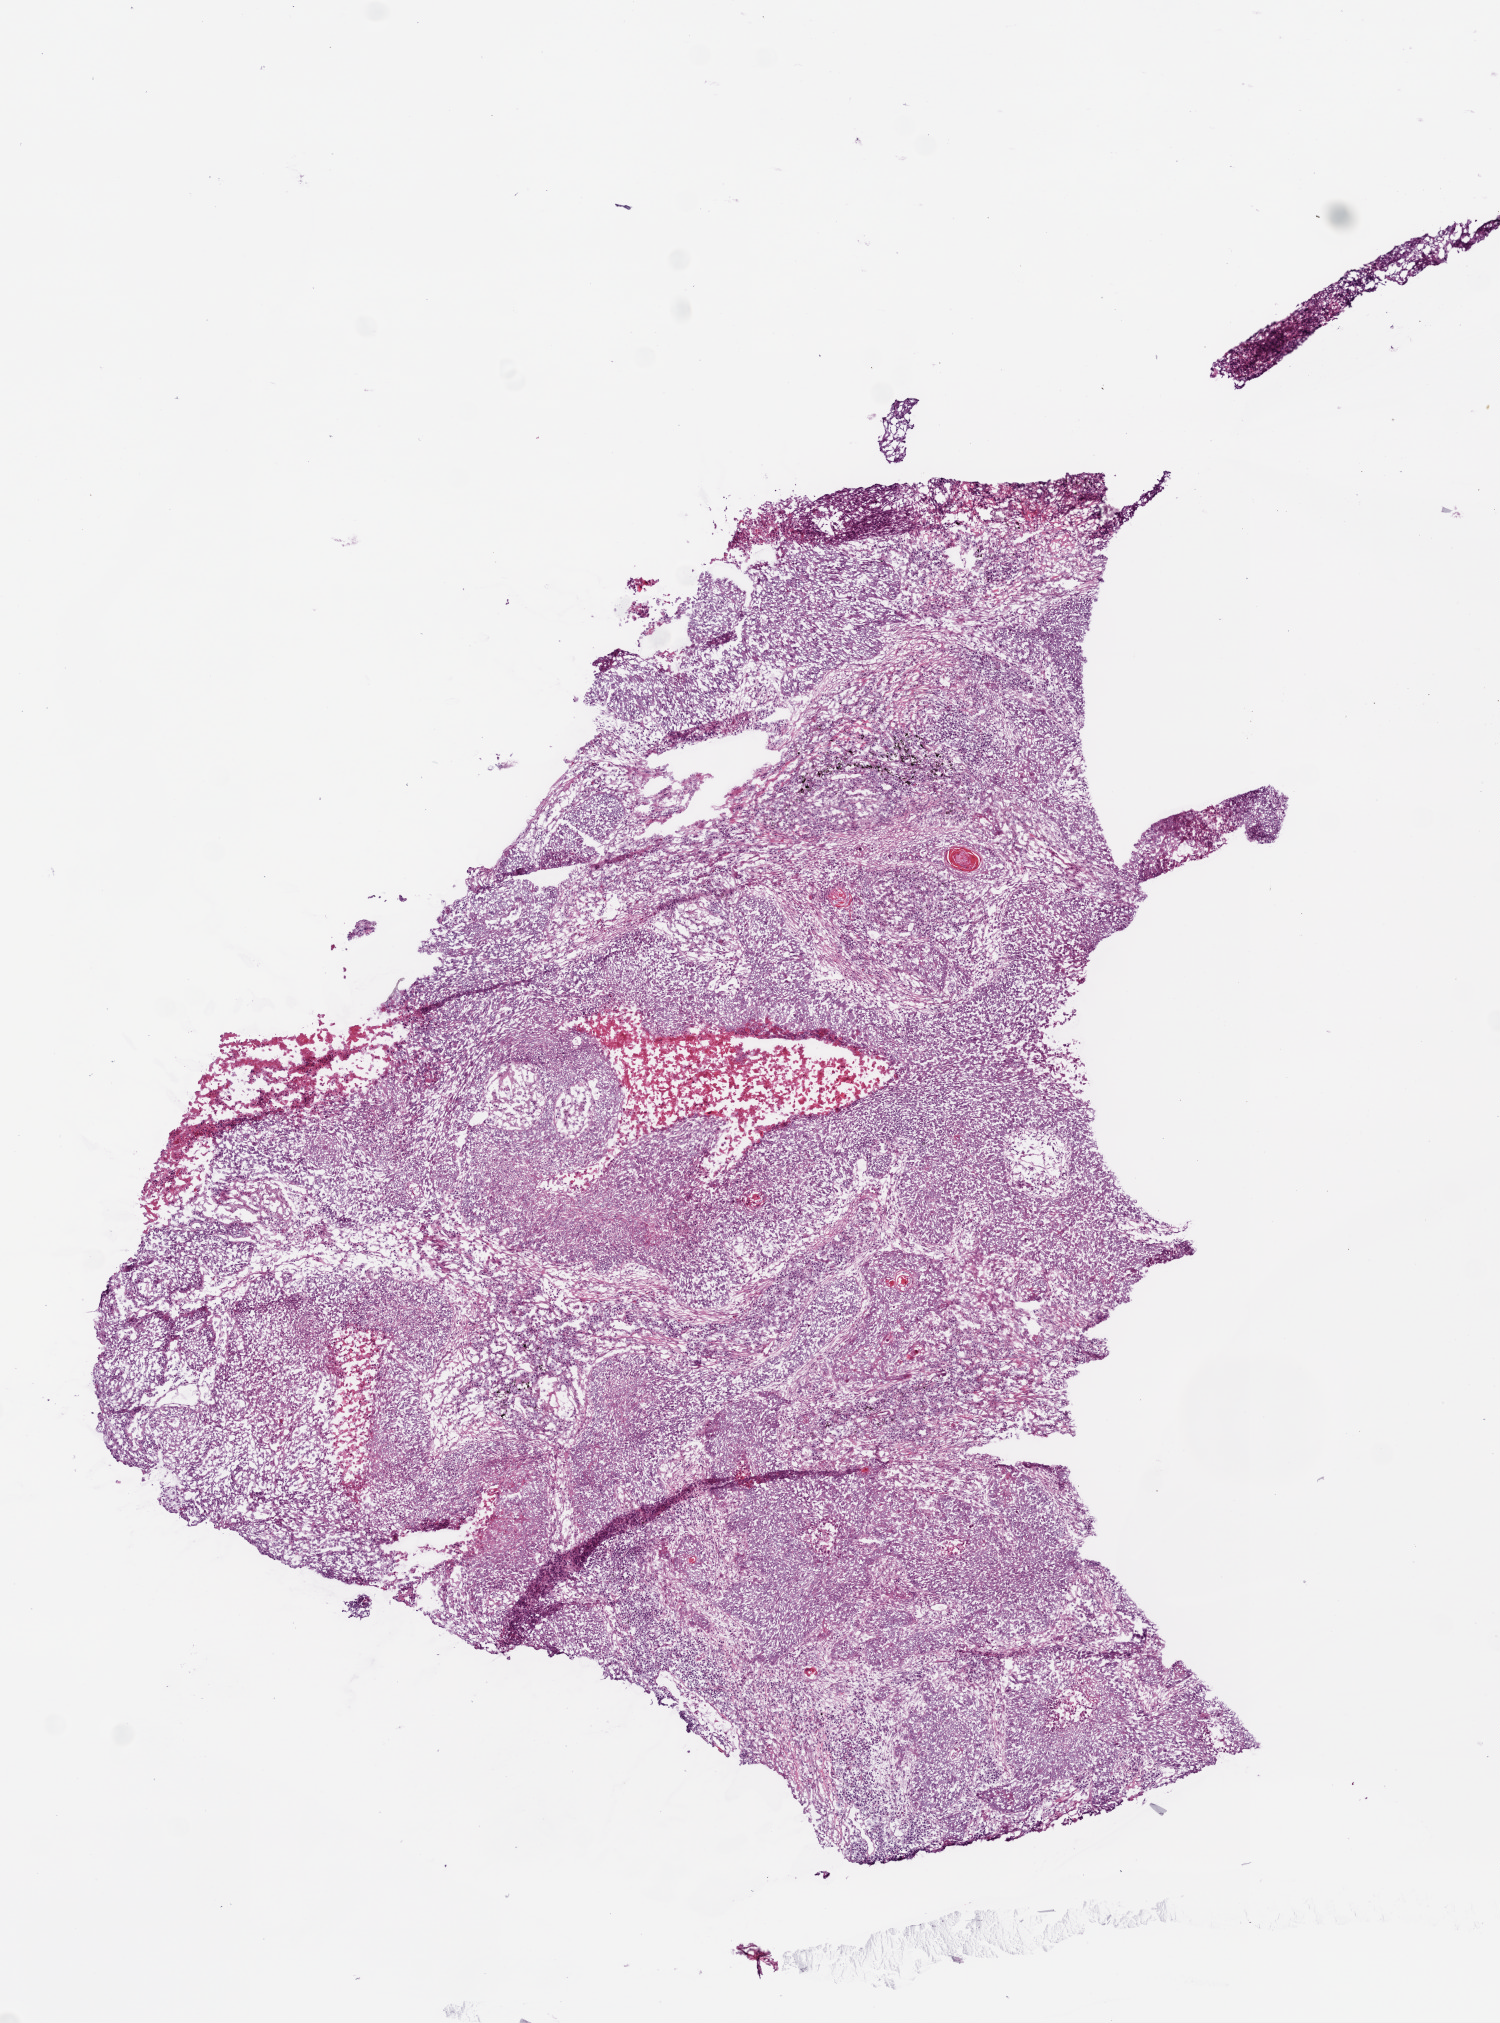
Digitized H&E tissue section (whole slide), a low-resolution overview of the entire scanned area, about 6.0 x 8.1 mm (slide scanned at 20x), frozen section from the bottom of the tissue portion, sample: primary tumour, lung. Male patient; age at initial diagnosis 64 years. Pathologist review of this section (percent, as recorded): tumour cells 75%, tumour nuclei 75%, normal cells 0%, stromal cells 15%, necrosis 10%.
AJCC pathologic stage: IB. TNM: T2 N0 M0. Pathologic diagnosis: Squamous cell carcinoma, NOS (lower lobe, lung).